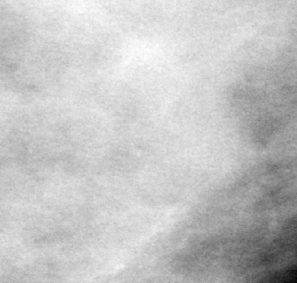
Cropped region of a digitized screen-film mammogram centred on a radiologist-marked abnormality, left breast, MLO view.
Mass, shape lobulated, margins obscured / ill defined; BI-RADS assessment category 3; pathology result (as recorded, not read from the image): malignant.